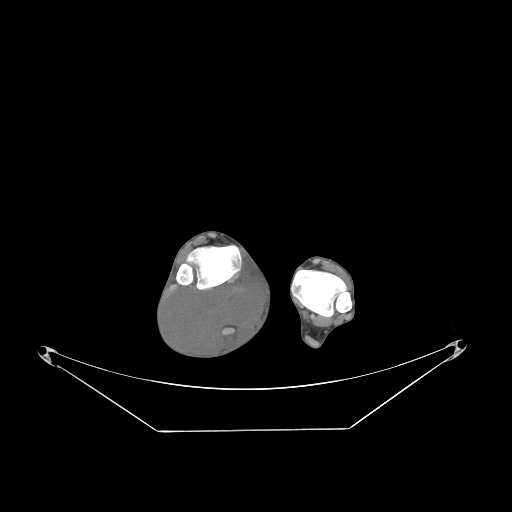
CT of an extremity soft-tissue mass (from a PET/CT study), one axial slice; slice 49 of 267 in the series (ordered by position); 140 kVp; soft-tissue window (W 400 / L 40 HU); 3.75 mm slice thickness; 512 × 512 image matrix, field of view 500 × 500 mm. Male patient. Case-level facts recorded for this patient, not image findings: histological type: liposarcoma - round cell; grade: high; site of the primary tumour: right calf.
Structures marked on this image (expert contour drawn on MRI and transferred to this co-registered scan by the dataset authors):
- gross tumour volume (mass): box from (x=165, y=274) to (x=266, y=357) px